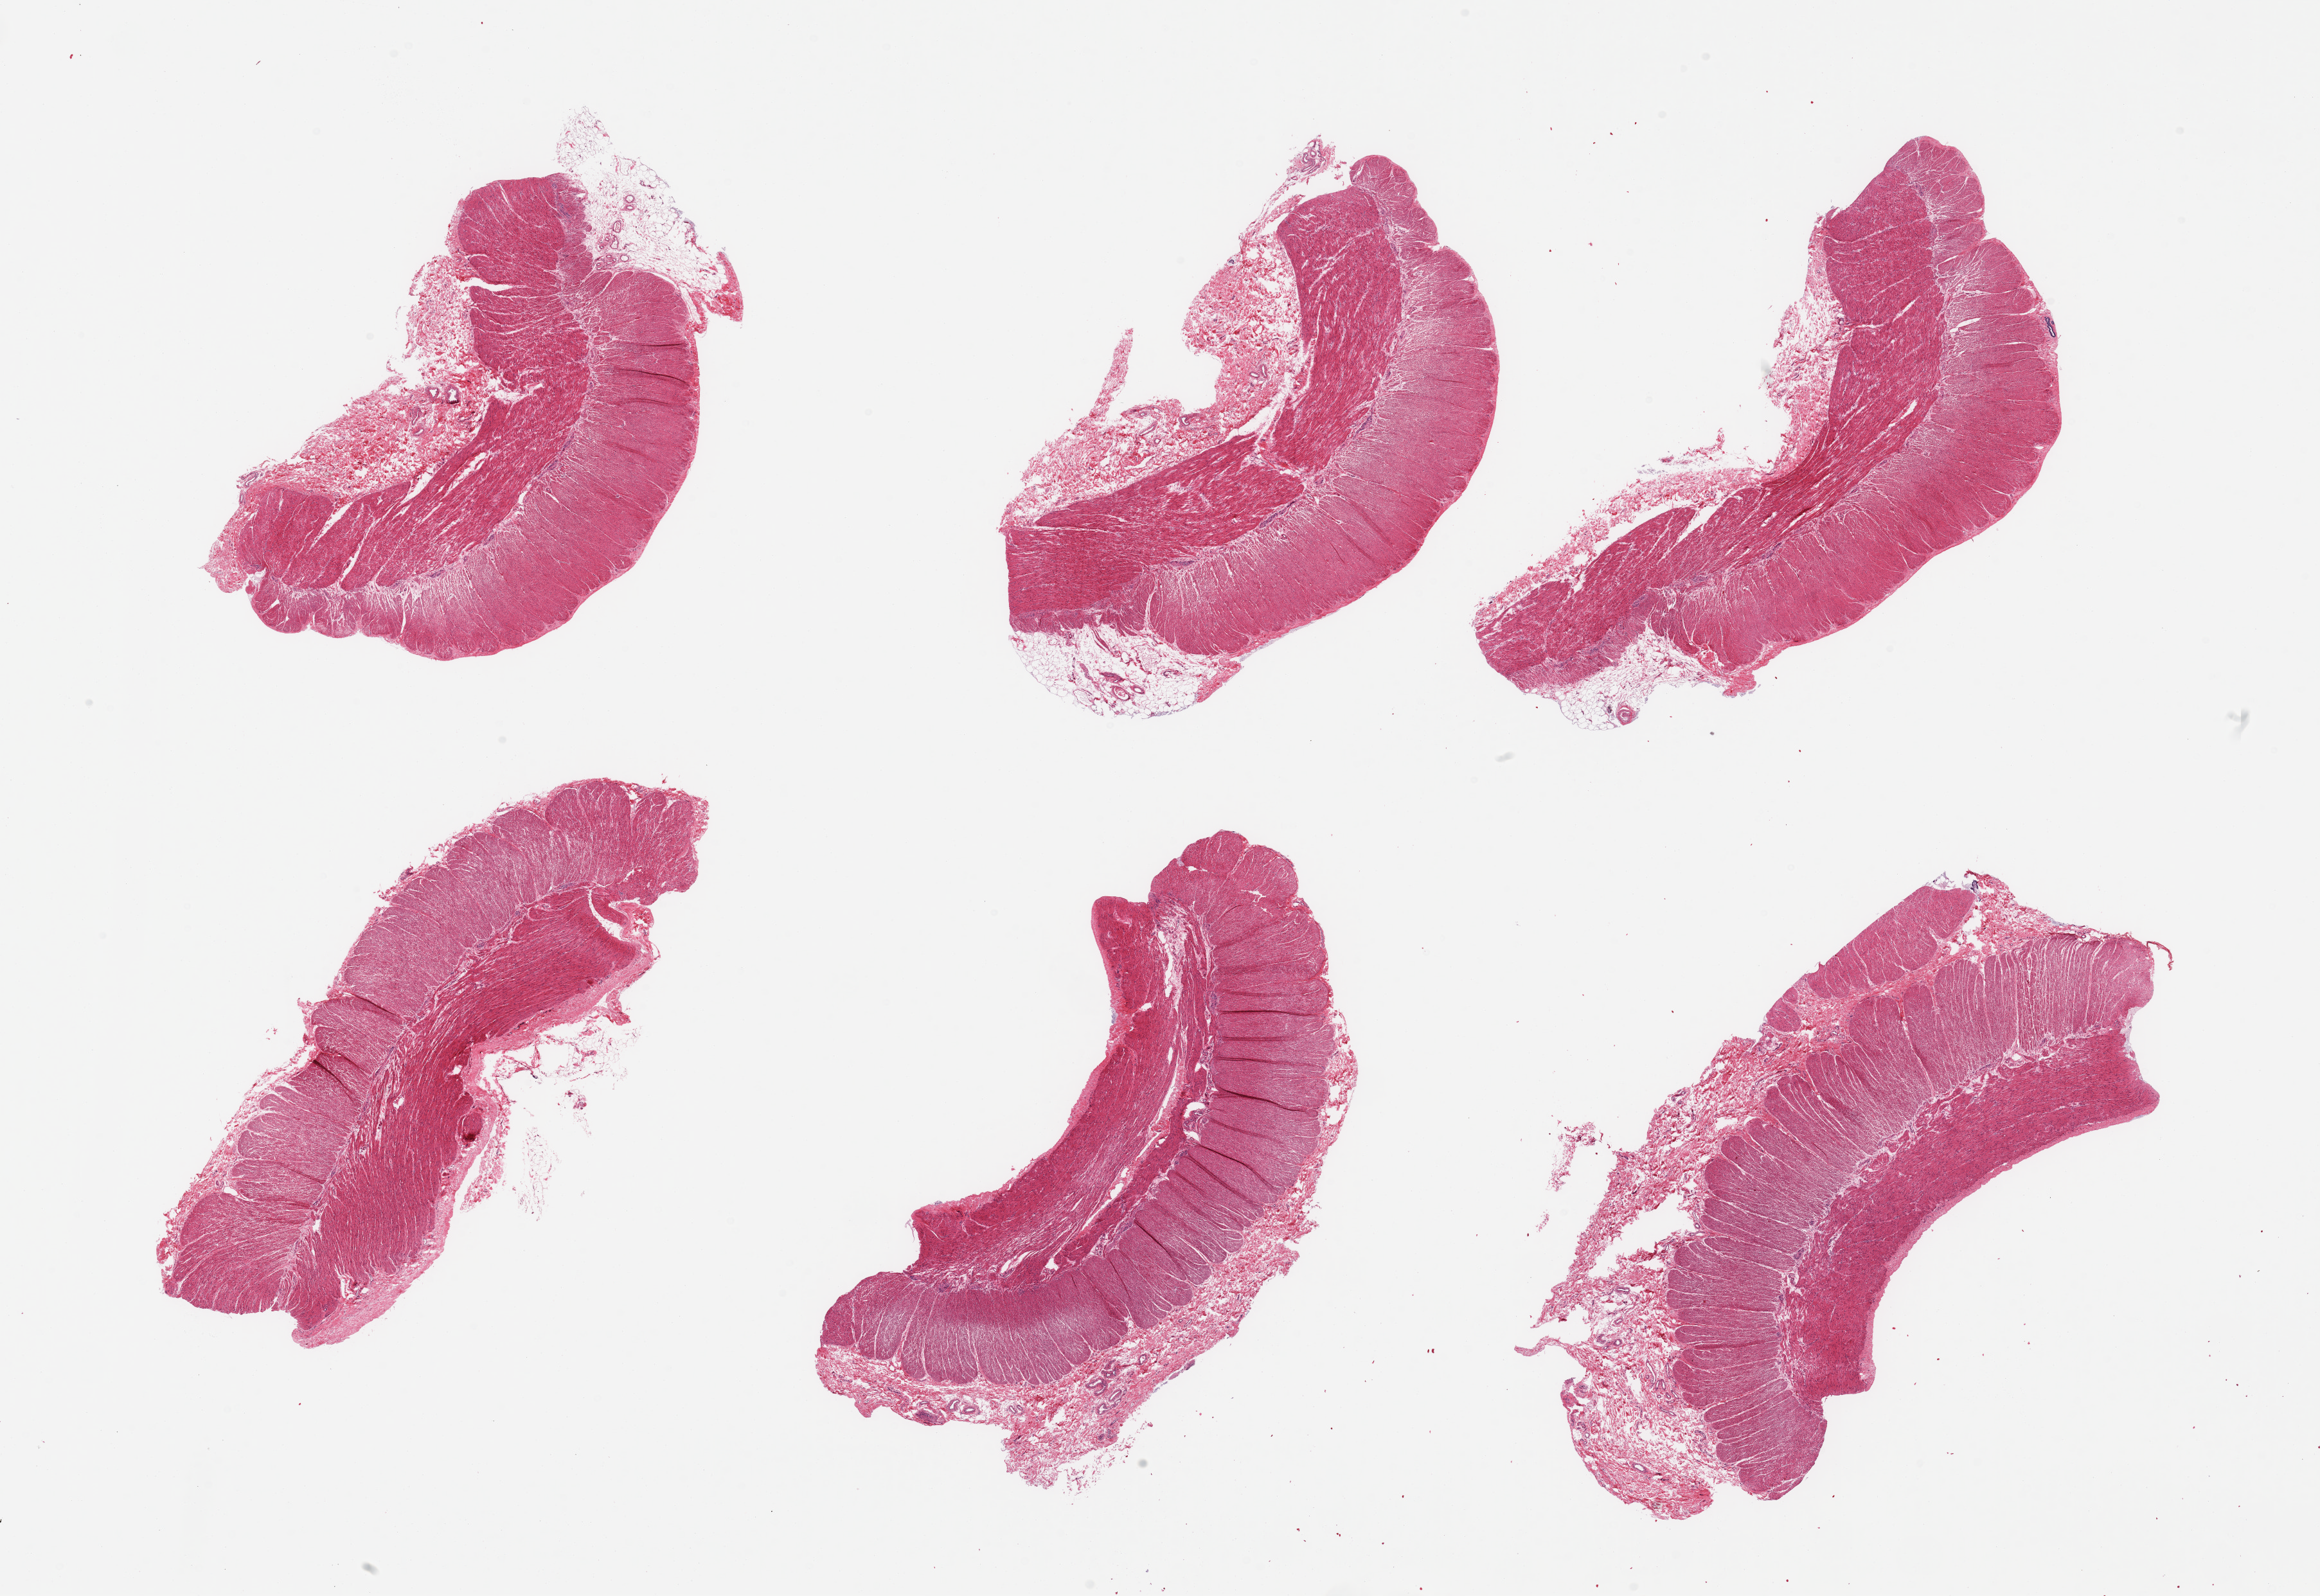
Whole-slide image, hematoxylin and eosin (H&E) stain, brightfield, shown as a low-resolution overview of the whole scanned area (about 28.5 x 19.6 mm); PAXgene-fixed paraffin-embedded (PFPE) section; target tissue: sigmoid colon; tissue donor sample. Donor: female.
• pathologist's review note for this sample: 6 pieces, confirmed target muscularis; adherent nubbins of fat, 1-2mm